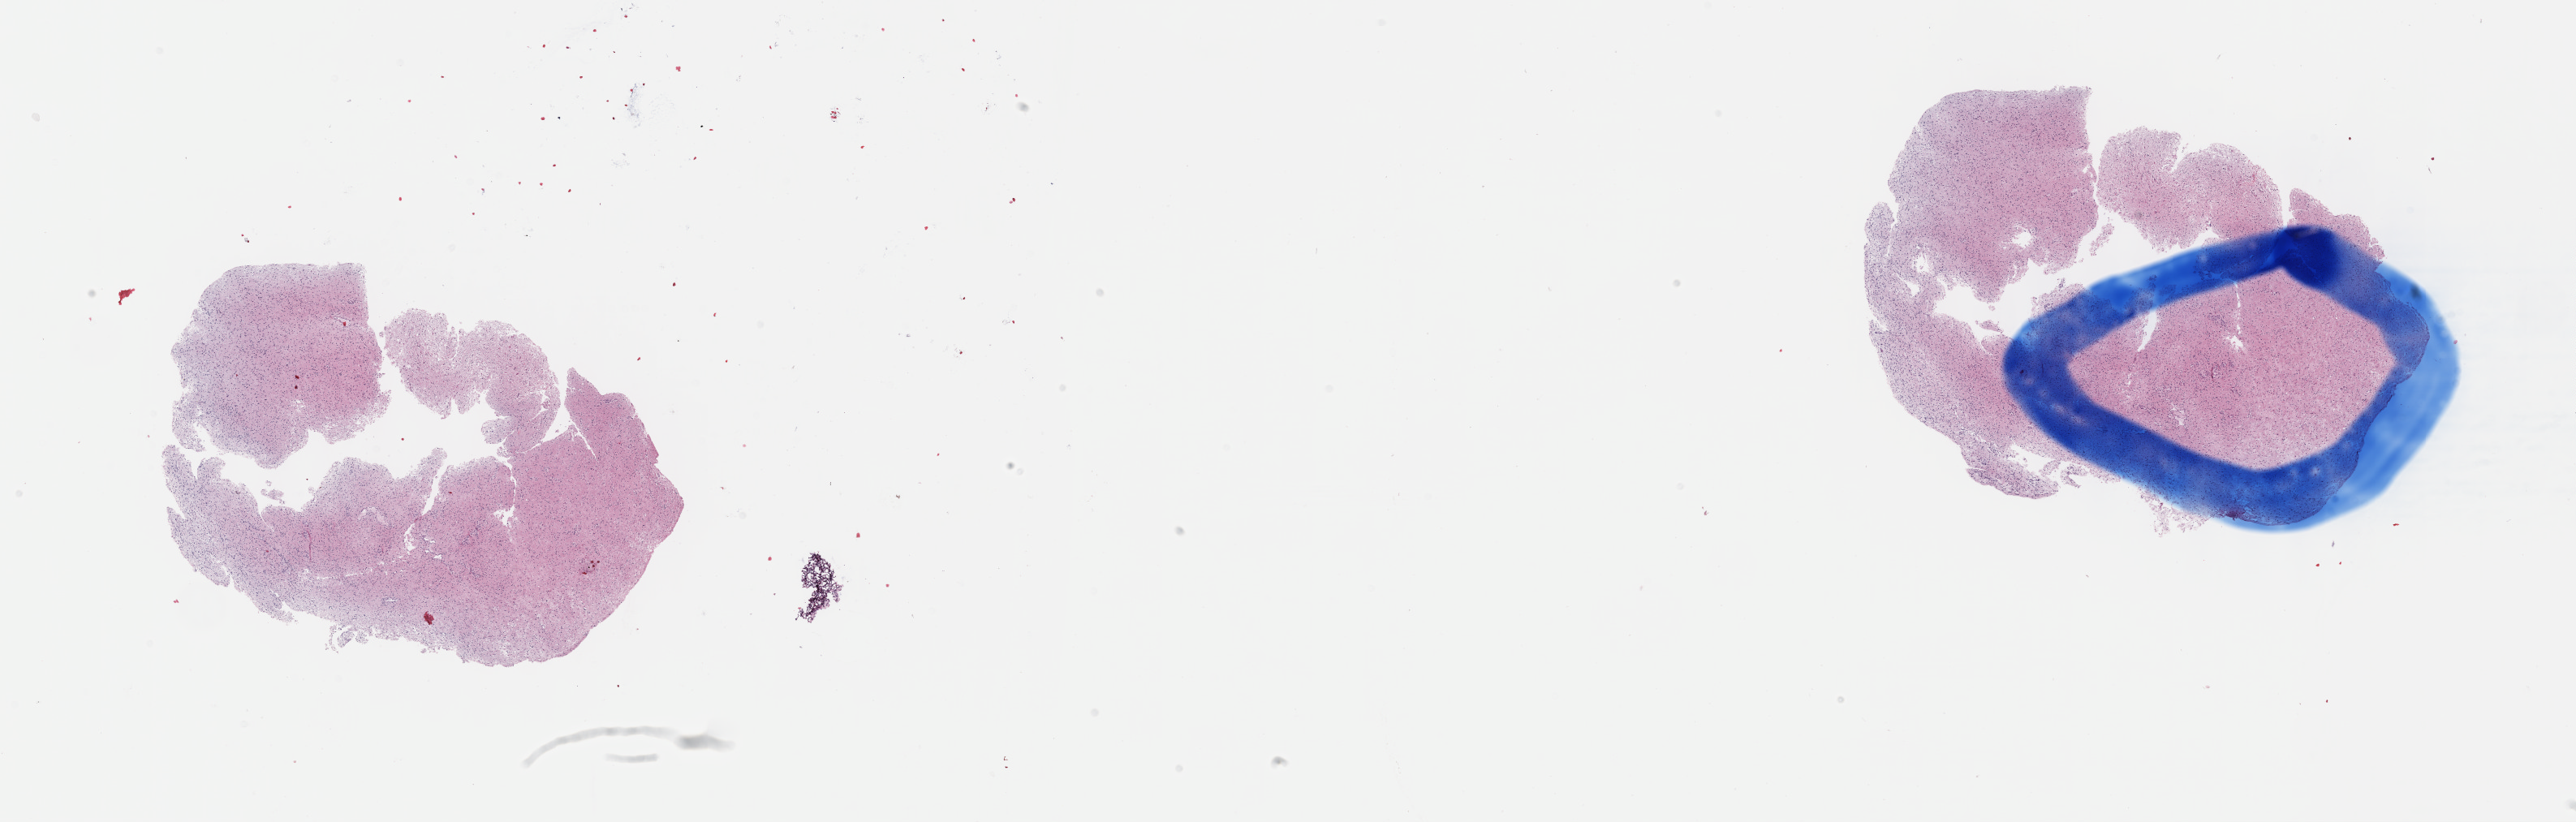
Digitized H&E-stained tissue section (whole slide), whole scanned area (about 25.7 x 8.2 mm) shown as a low-resolution overview. FFPE section. Primary tumour sample from the brain. Female patient; age at initial diagnosis 53 years. Histologic grade: G3 (poorly differentiated).
Histologic diagnosis: Mixed glioma (cerebrum).